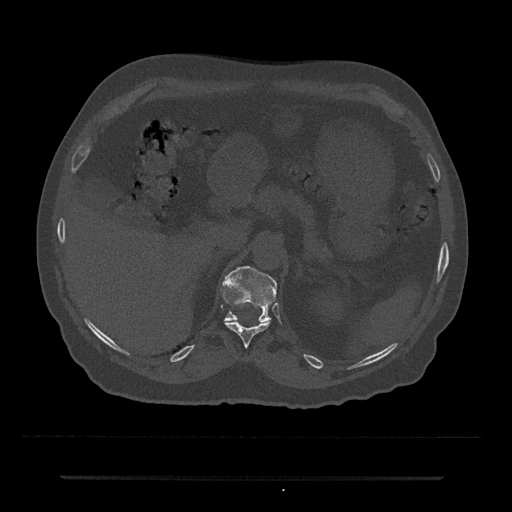
CT including the spine, one axial slice. Position 161 of 797 along the scan axis. Bone window (W 1800 / L 400 HU). 0.5 mm slice thickness. 512 × 512 image matrix, field of view 437 × 437 mm. Patient: male, 69 years. Case-level facts recorded for this patient, not image findings: primary cancer: prostate.
Annotated regions visible in this slice (semi-automatically segmented with operator editing):
- T11 vertebra: box from (x=225, y=321) to (x=270, y=347) px
- T12 vertebra: (x=224, y=265)–(x=277, y=322)